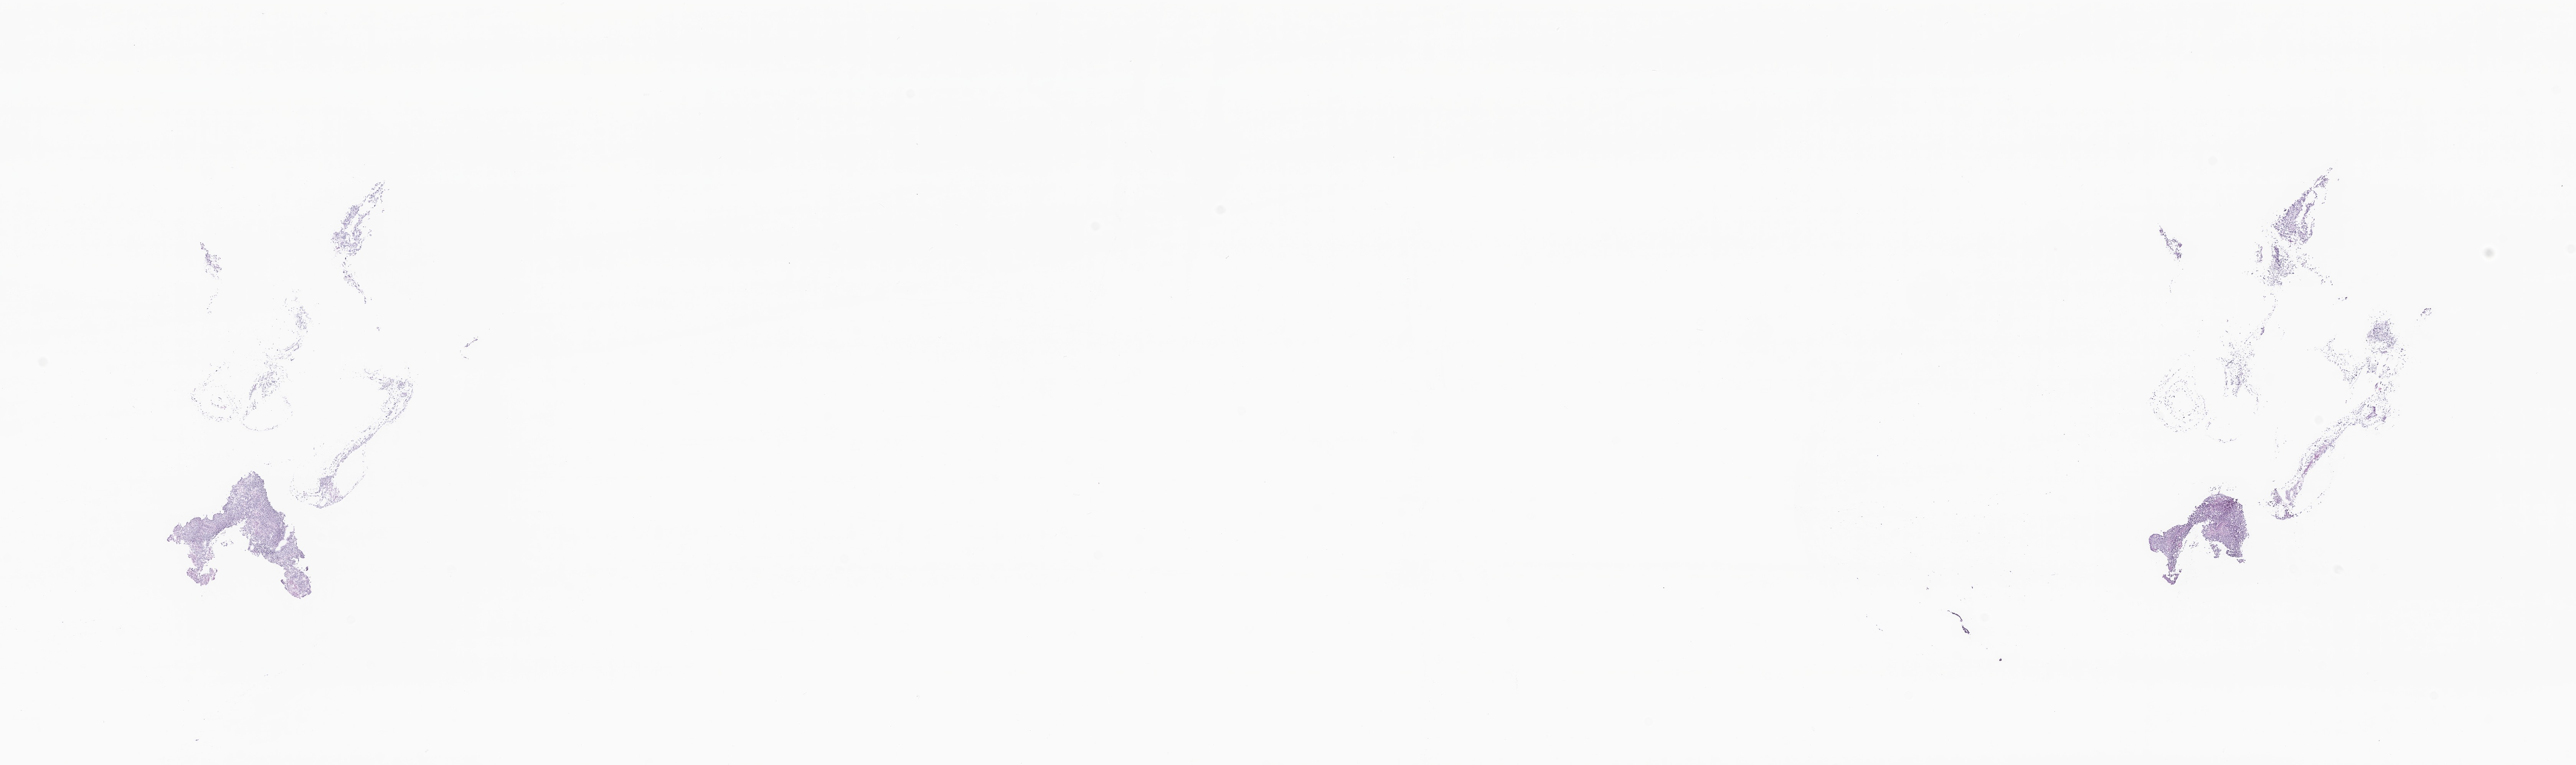
Whole-slide image, hematoxylin and eosin (H&E) stain of tumor tissue from the brain — whole scanned area (about 28.3 x 8.4 mm) shown as a low-resolution overview; cryosection (OCT / tissue freezing medium). Male patient, age 70 months (5 years 10 months).
• recorded diagnosis: Medulloblastoma, NOS